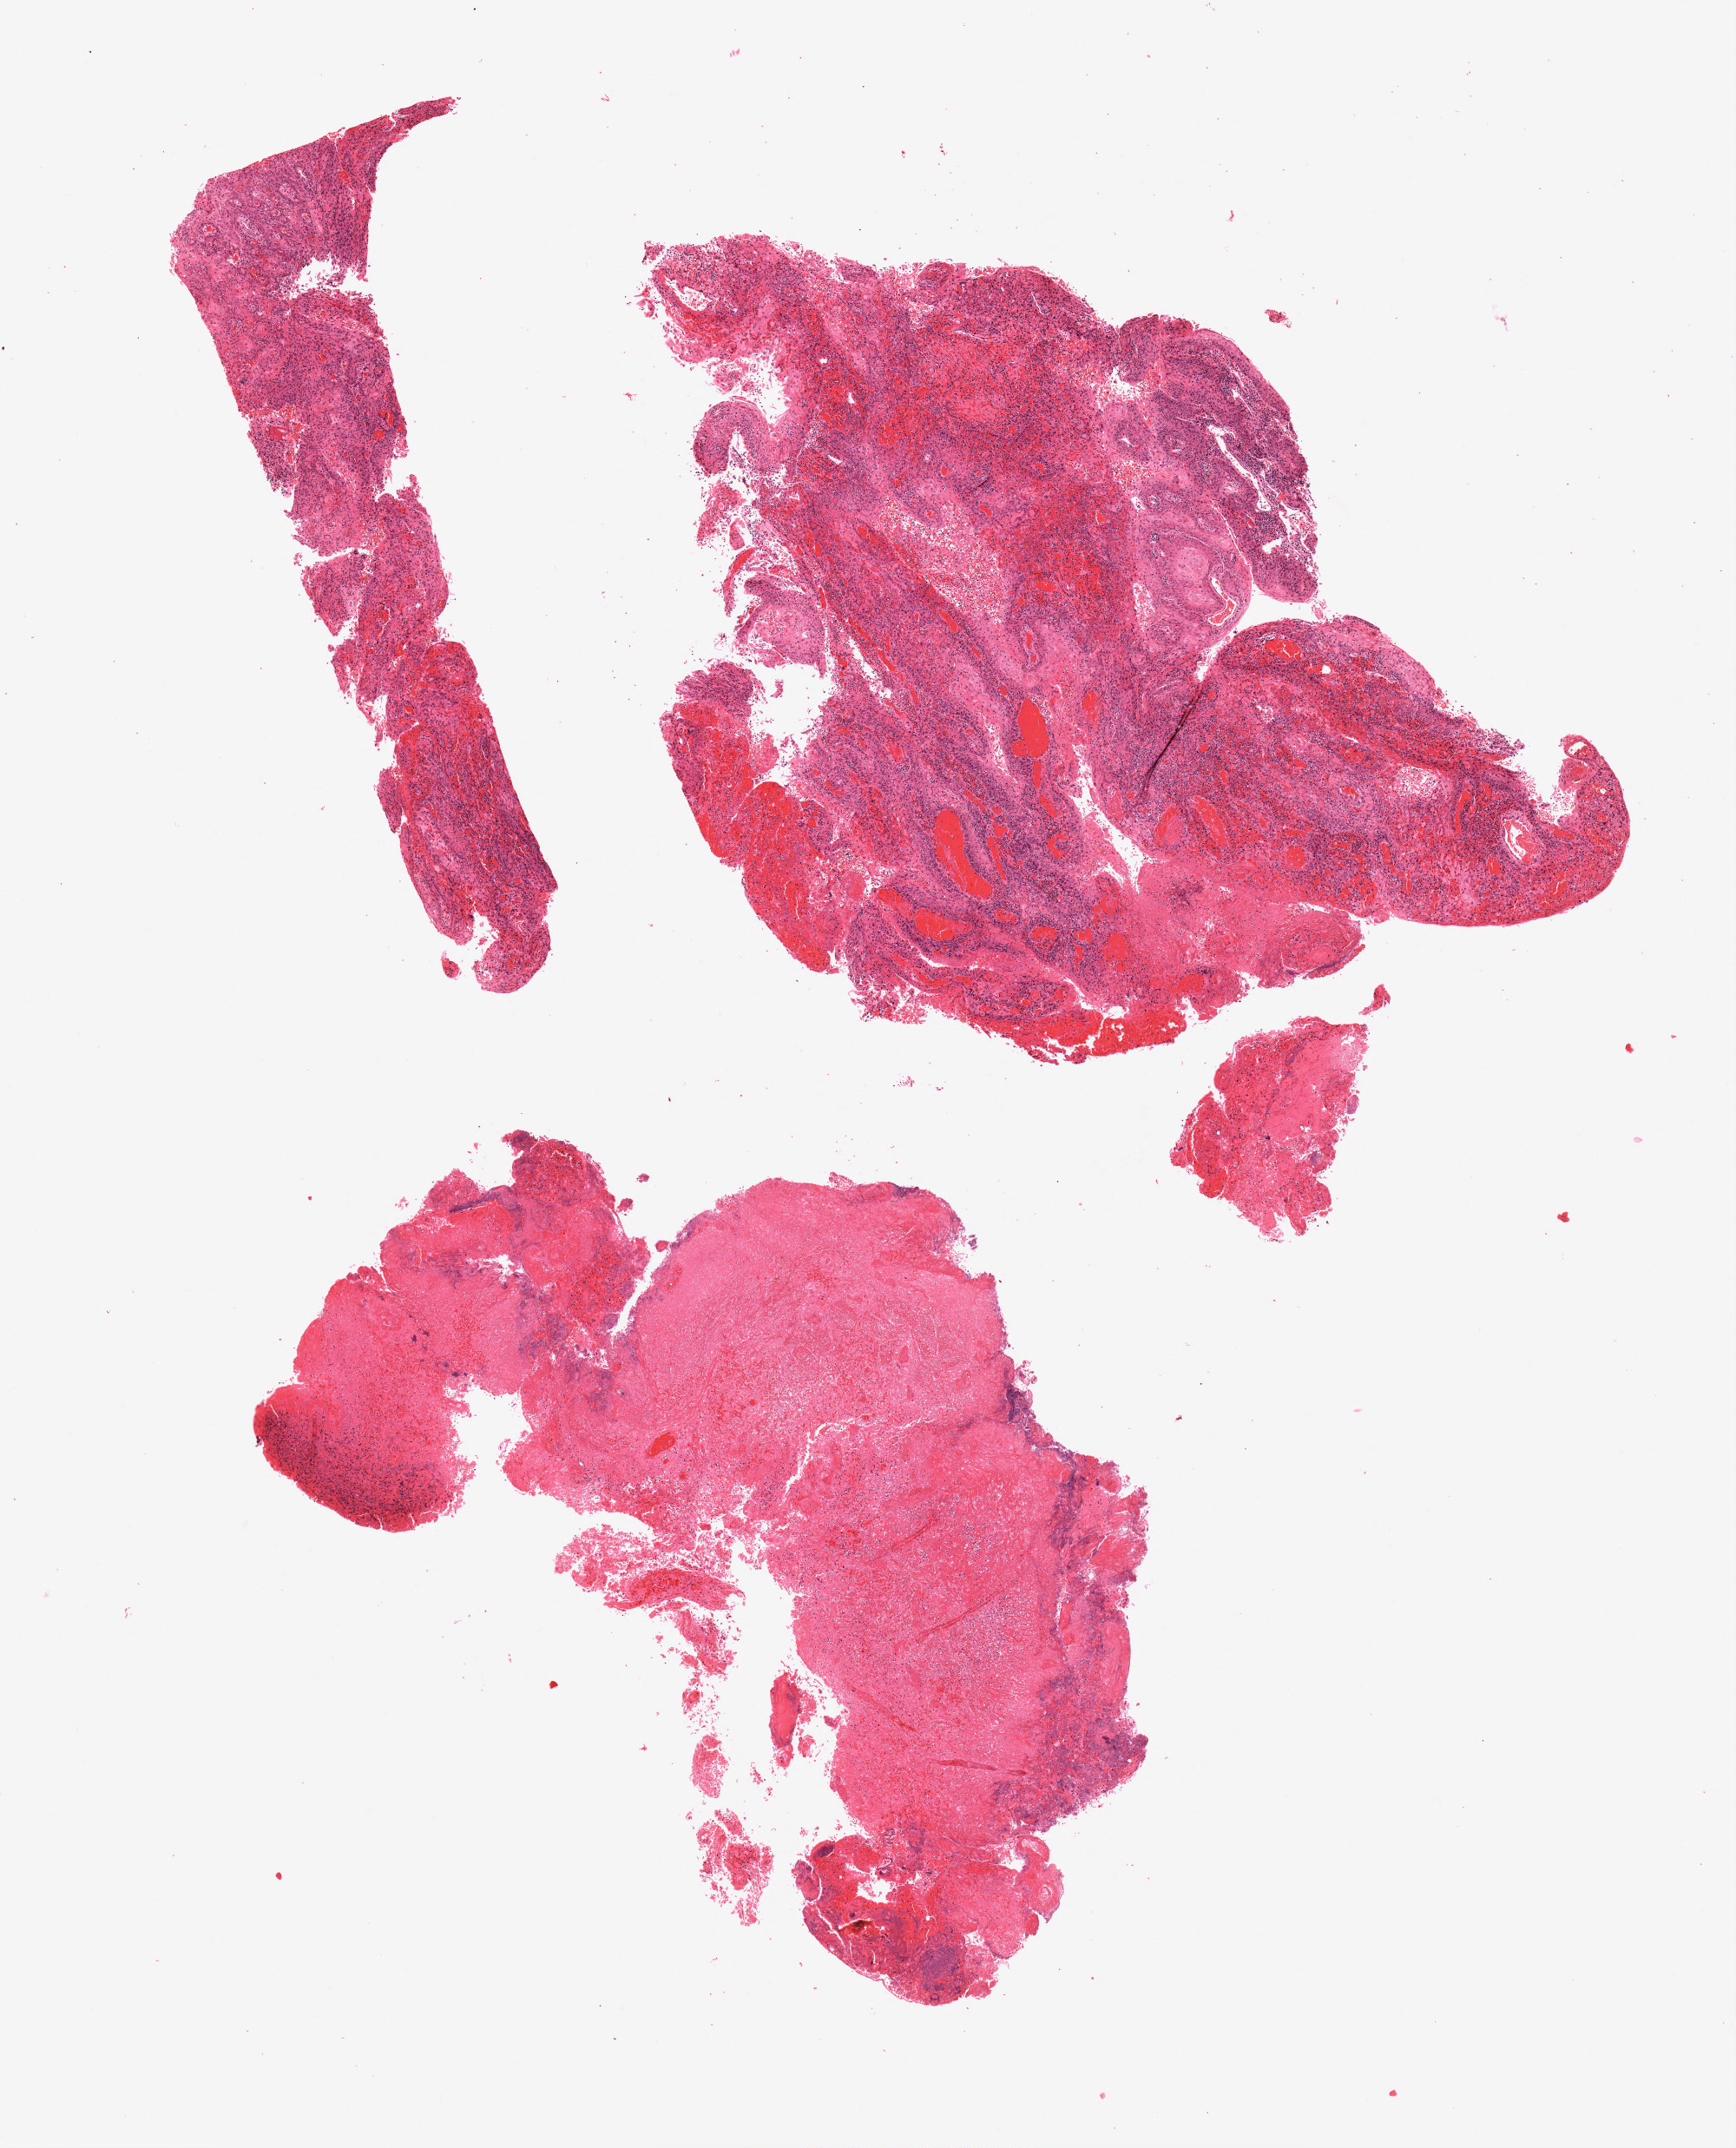
Digitized H&E tissue section (whole slide) — whole scanned area (about 8.0 x 9.9 mm, slide scanned at 20x) shown as a low-resolution overview. FFPE section. Primary tumour sample from the head and neck. Female, age 60 years at initial diagnosis. Histologic grade: G2 (moderately differentiated).
• pathologic diagnosis: Squamous cell carcinoma, keratinizing, NOS
• AJCC pathologic stage: IVA
• lymph nodes positive (case pathology): 0 of 64 examined
• laterality: right